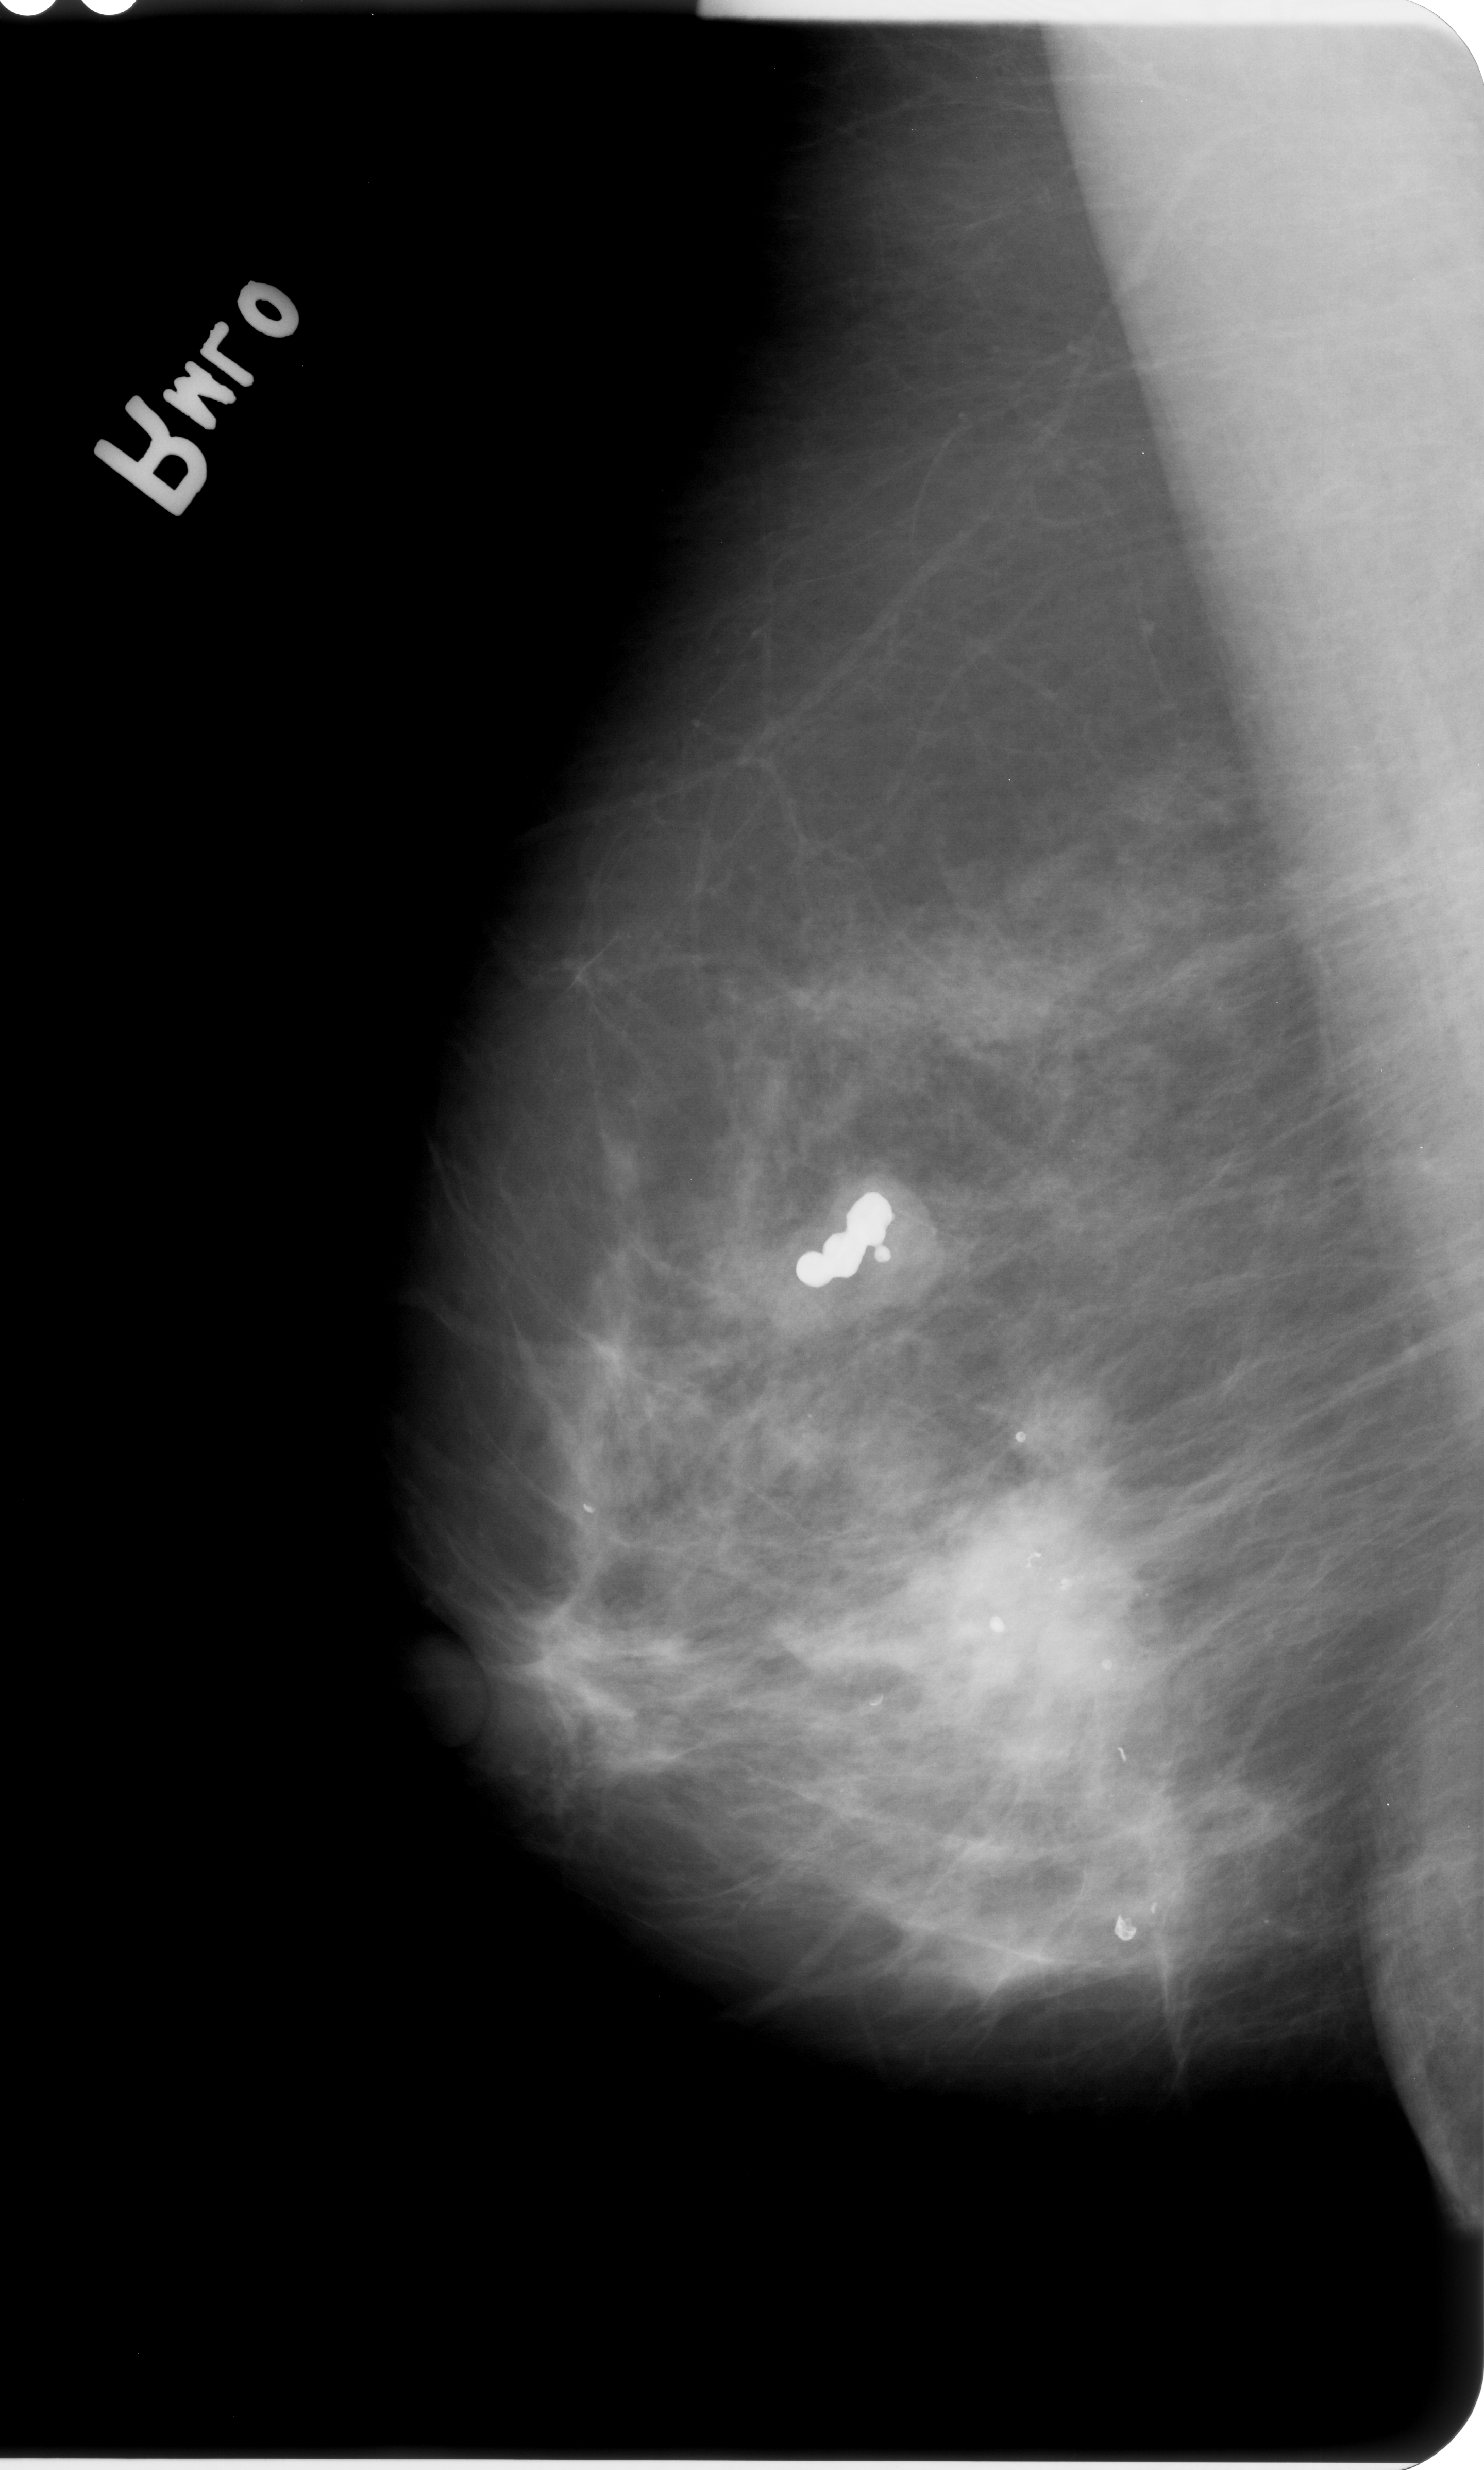
Digitized screen-film mammogram. Right breast. MLO view. BI-RADS breast density category 3 (scale 1–4). 1484 × 2470 image matrix.
Expert-marked regions of interest on this image (one box per marked abnormality):
- Finding 1 of 2: calcifications, morphology pleomorphic, distribution clustered; BI-RADS assessment category 4; pathology (as recorded): malignant: box from (x=1026, y=1542) to (x=1048, y=1576) px
- Finding 2 of 2: calcifications, morphology pleomorphic, distribution clustered; BI-RADS assessment category 4; pathology result (as recorded, not read from the image): malignant: (x=1059, y=1566)–(x=1081, y=1597)